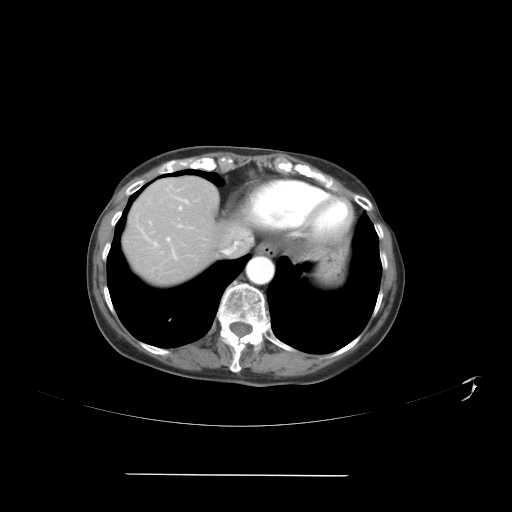
Contrast-enhanced abdominal CT, one axial slice; position 34 of 41 along the scan axis; 120 kVp; intravenous contrast given; soft-tissue window (W 400 / L 40 HU); 5 mm slice thickness; 512 × 512 image matrix, field of view 431 × 431 mm. Female patient, age 74 years. From the clinical record (not read from this slice): diagnosis: colorectal cancer liver metastases, imaged before liver resection; multiple liver metastases: yes; largest metastasis: 3.3 cm; disease in both lobes: yes.
Outlined on this slice (expert manual segmentation):
- liver: bounding box (x1, y1, x2, y2) in pixels: (125, 177, 242, 284)
- planned liver remnant (the part of the liver to remain after resection): (127, 177, 242, 253)
- portal vein (with intrahepatic branches): (166, 207, 182, 241)